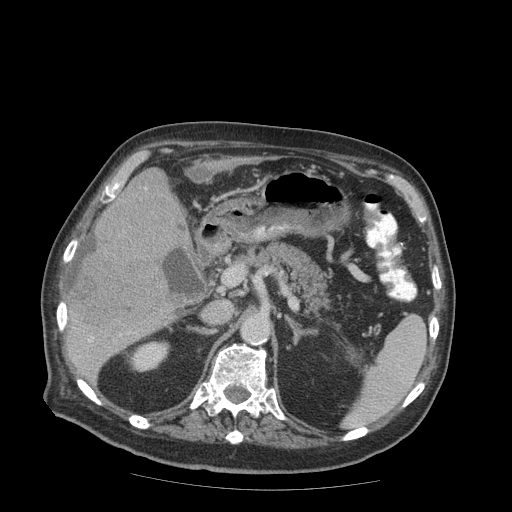
Contrast-enhanced abdominal CT (liver protocol), one axial slice. Reconstruction kernel STANDARD. Soft-tissue window (W 400 / L 40 HU). 2.5 mm slice thickness. 512 × 512 image matrix, field of view 420 × 420 mm. From the clinical record (not read from this slice): diagnosis: hepatocellular carcinoma (patient treated with transarterial chemoembolisation; whether this scan precedes or follows treatment is not stated here); TNM stage (as recorded): Stage-IIIB; Child-Pugh class: A; tumour differentiation: well differentiated; tumour nodularity: multinodular.
Structures marked on this image (semi-automatic segmentation, software-assisted and operator-edited):
- liver parenchyma outside the tumour (the mass and vessels are separate outlines, so this box may not span the whole liver): bounding box <68,168,186,380> (left, top, right, bottom; pixels)
- mass: <71,192,188,327>
- liver vessels: <88,335,121,342>